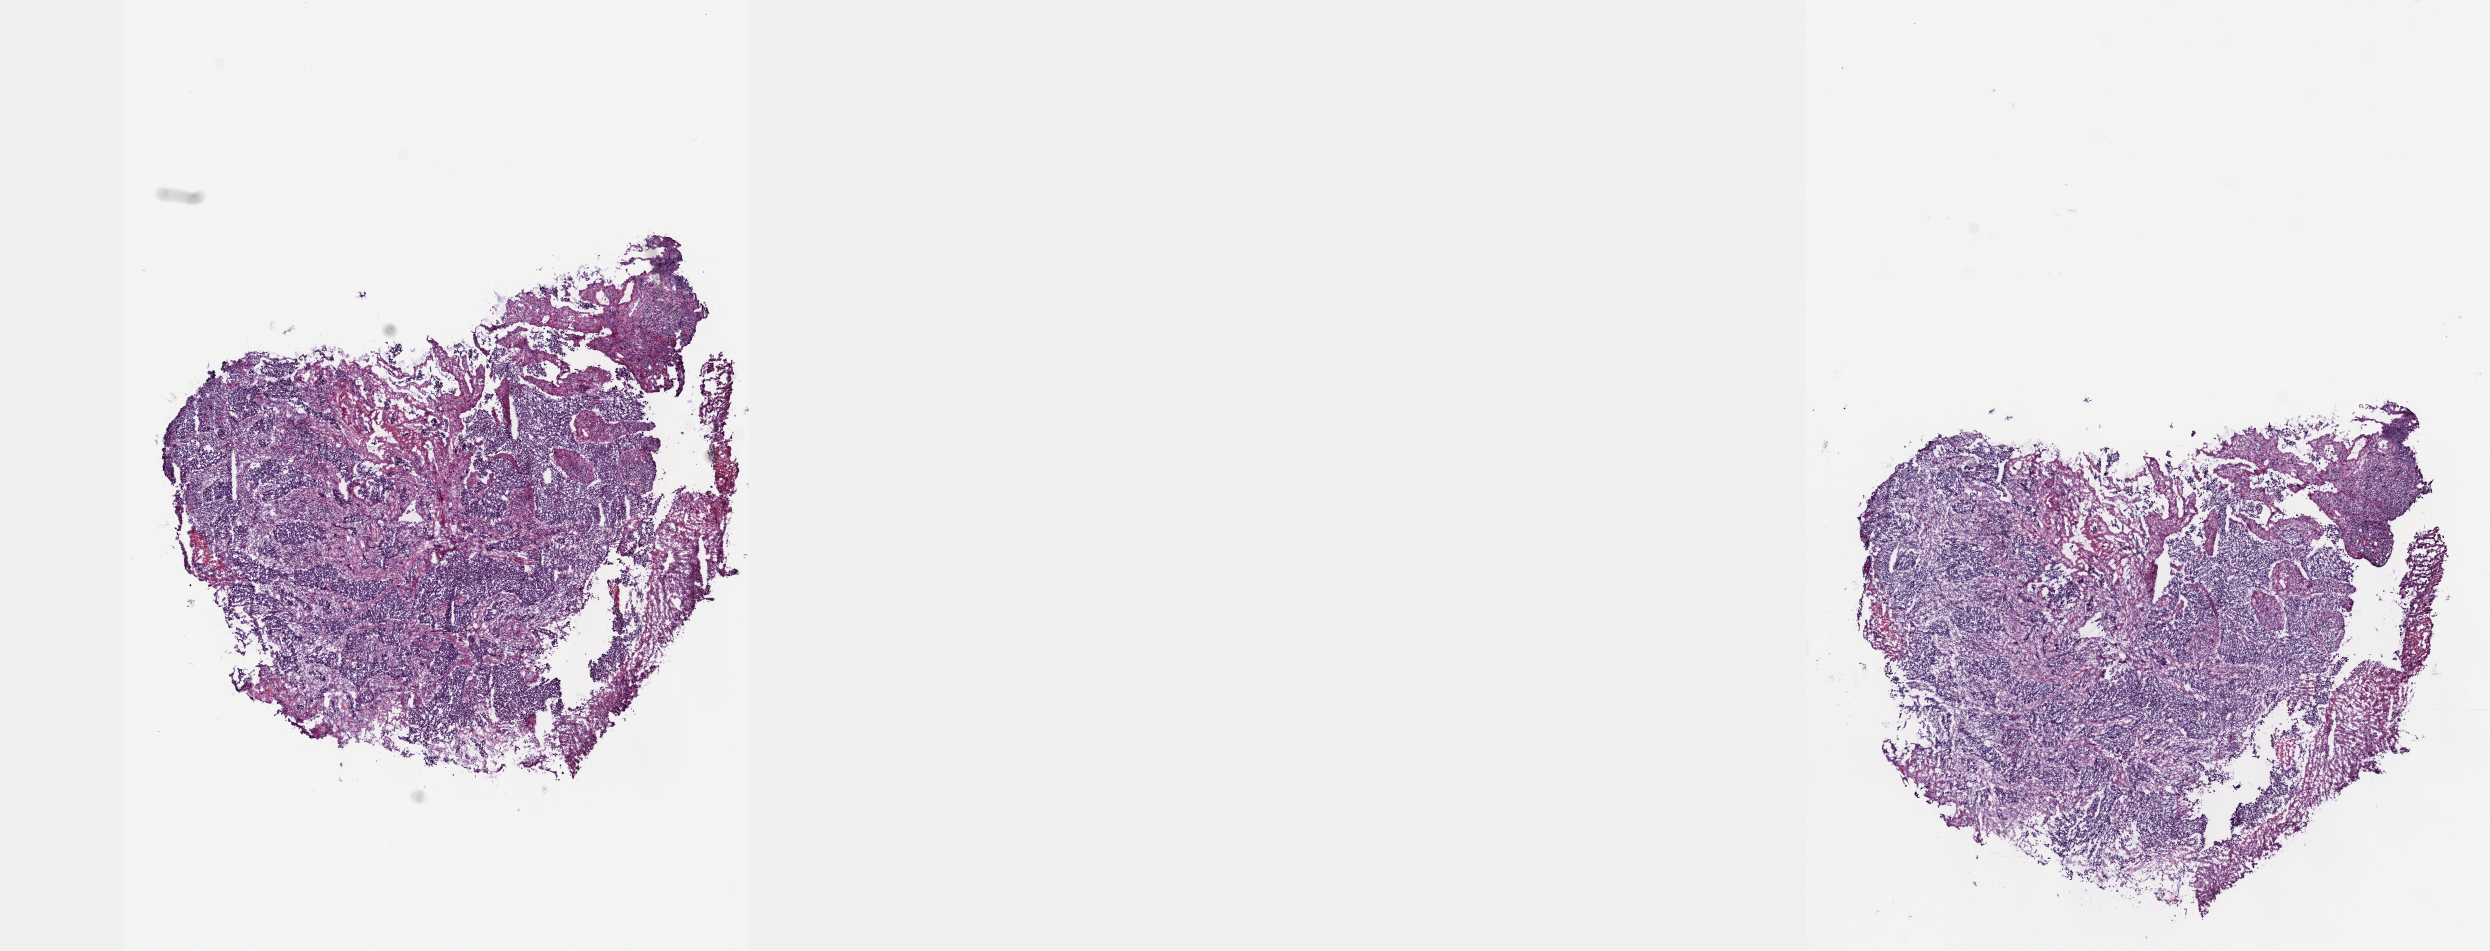
Whole-slide histology image, Hematoxylin and eosin (H&E) stained, low-resolution overview of the scanned area, about 20.1 x 7.7 mm (acquisition: 40x scan), frozen section from the top of the tissue portion, cervix, primary tumour sample. Female patient; age at initial diagnosis 43 years. Histologic grade: G3 (poorly differentiated). Pathologist review of this section (percent, as recorded): tumour cells 70%, tumour nuclei 70%, normal cells 0%, stromal cells 25%, necrosis 5%. Infiltration values recorded for this section: lymphocyte infiltration 50%, monocyte infiltration 20%, neutrophil infiltration 20%.
FIGO stage: IIA. Pathologic diagnosis: Mucinous adenocarcinoma, endocervical type (cervix uteri).